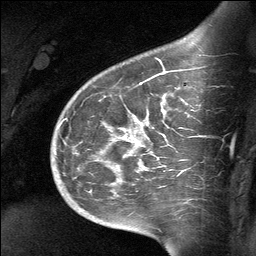
Breast MRI (dynamic contrast-enhanced), one sagittal slice. Position 47 of 64 along the scan axis. Dynamic contrast-enhanced study with each time point stored as its own series, time point 2 of 3 at this slice position (early post-contrast, ordered by acquisition time). 1.5 T. TE 4.8 ms, TR 27 ms. 2 mm slice thickness. 256 × 256 image matrix, field of view 200 × 200 mm. Female patient, age 39 years. From the clinical record (not read from this slice): setting: breast cancer imaged before/during neoadjuvant chemotherapy; receptor status: HER2-positive.
Annotated regions visible in this slice (semi-automatically segmented with operator editing):
- analysis volume of interest (the breast-tissue region the enhancement analysis was run in; not a lesion): bounding box (x1, y1, x2, y2) in pixels: (70, 69, 202, 224)
- tumour enhancement mask (voxels above the 90 % enhancement threshold inside the analysis volume of interest): (122, 72, 165, 140)